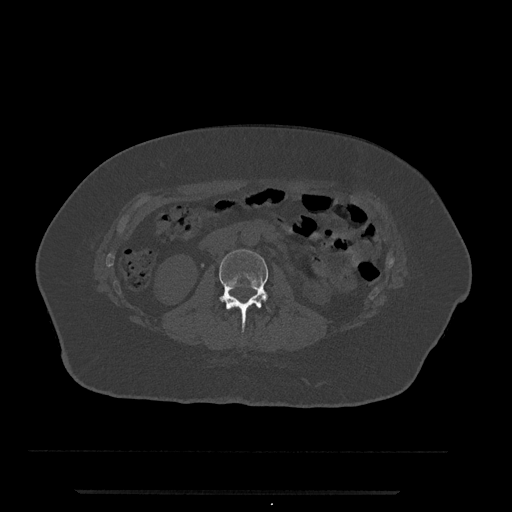
CT including the spine, one axial slice; slice 34 of 797 in the series (ordered by position); reconstruction kernel Br40s/3; 120 kVp; bone window (W 1800 / L 400 HU); 0.5 mm slice thickness; 512 × 512 image matrix, field of view 440 × 440 mm. Patient: female, 51 years. Case-level facts recorded for this patient, not image findings: primary cancer: neuro; vertebrae with lytic lesions (as recorded): T8.
Outlined on this slice (semi-automatic segmentation, software-assisted and operator-edited):
- L2 vertebra: bounding box [x1, y1, x2, y2] px = [219, 249, 269, 329]